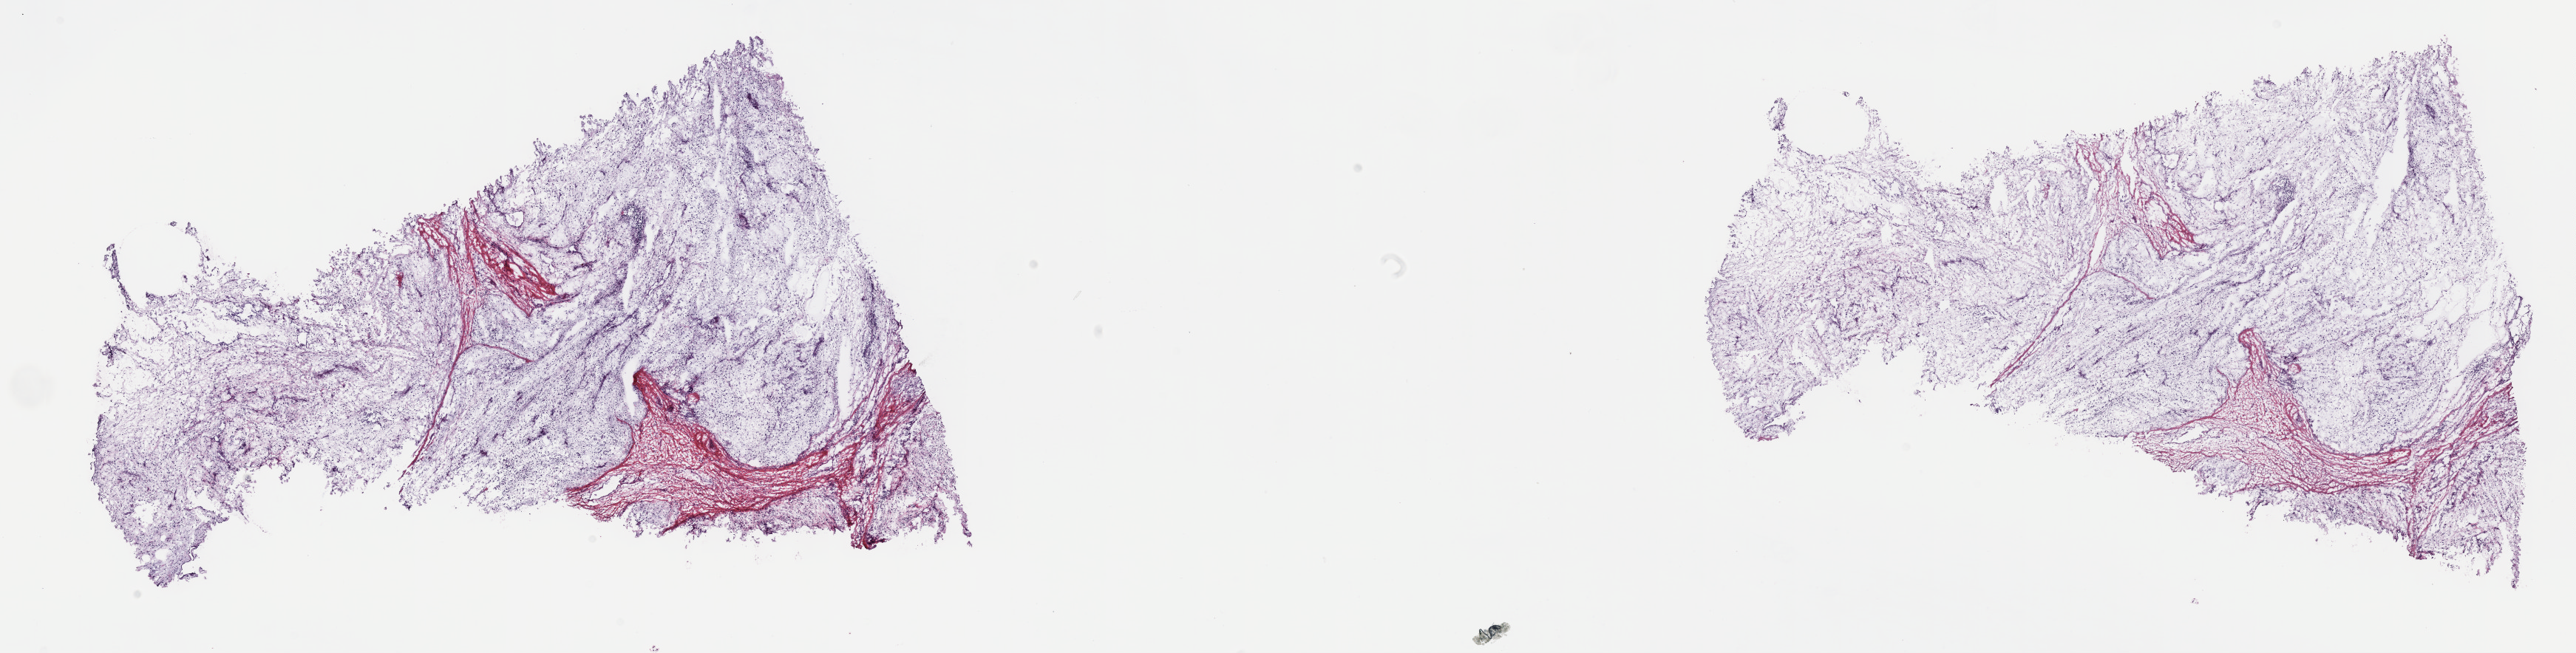
Digitized H&E tissue section (whole slide) — shown as a low-resolution overview of the whole scanned area (about 28.2 x 7.2 mm, slide scanned at 40x), frozen section, primary tumour sample from the testis. Male patient; age at initial diagnosis 27 years. Composition of this section per pathologist review: tumour cells 90%, tumour nuclei 90%, normal cells 0%, stromal cells 10%, necrosis 0%. Infiltration values recorded for this section: lymphocyte infiltration 5%, monocyte infiltration 0%, neutrophil infiltration 0%.
AJCC pathologic stage: IS. Laterality: right. Pathologic diagnosis: Teratocarcinoma.